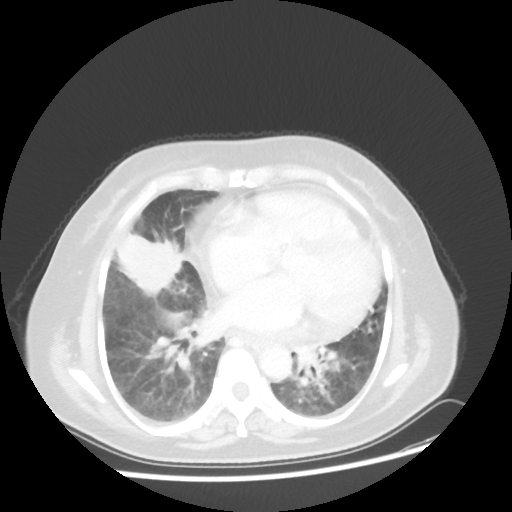
Chest CT, one axial slice. Position 19 of 45 along the scan axis. Lung window (W 1500 / L -600 HU). 5 mm slice thickness. 512 × 512 image matrix. Female patient, age 67 years. From the clinical record (not read from this slice): clinical TNM (as recorded): T2a N3 M1a.
Annotated regions visible in this slice (rectangle marked by the reading radiologist):
- lung tumour (recorded histology: adenocarcinoma): bounding box [x1, y1, x2, y2] px = [115, 231, 184, 297]